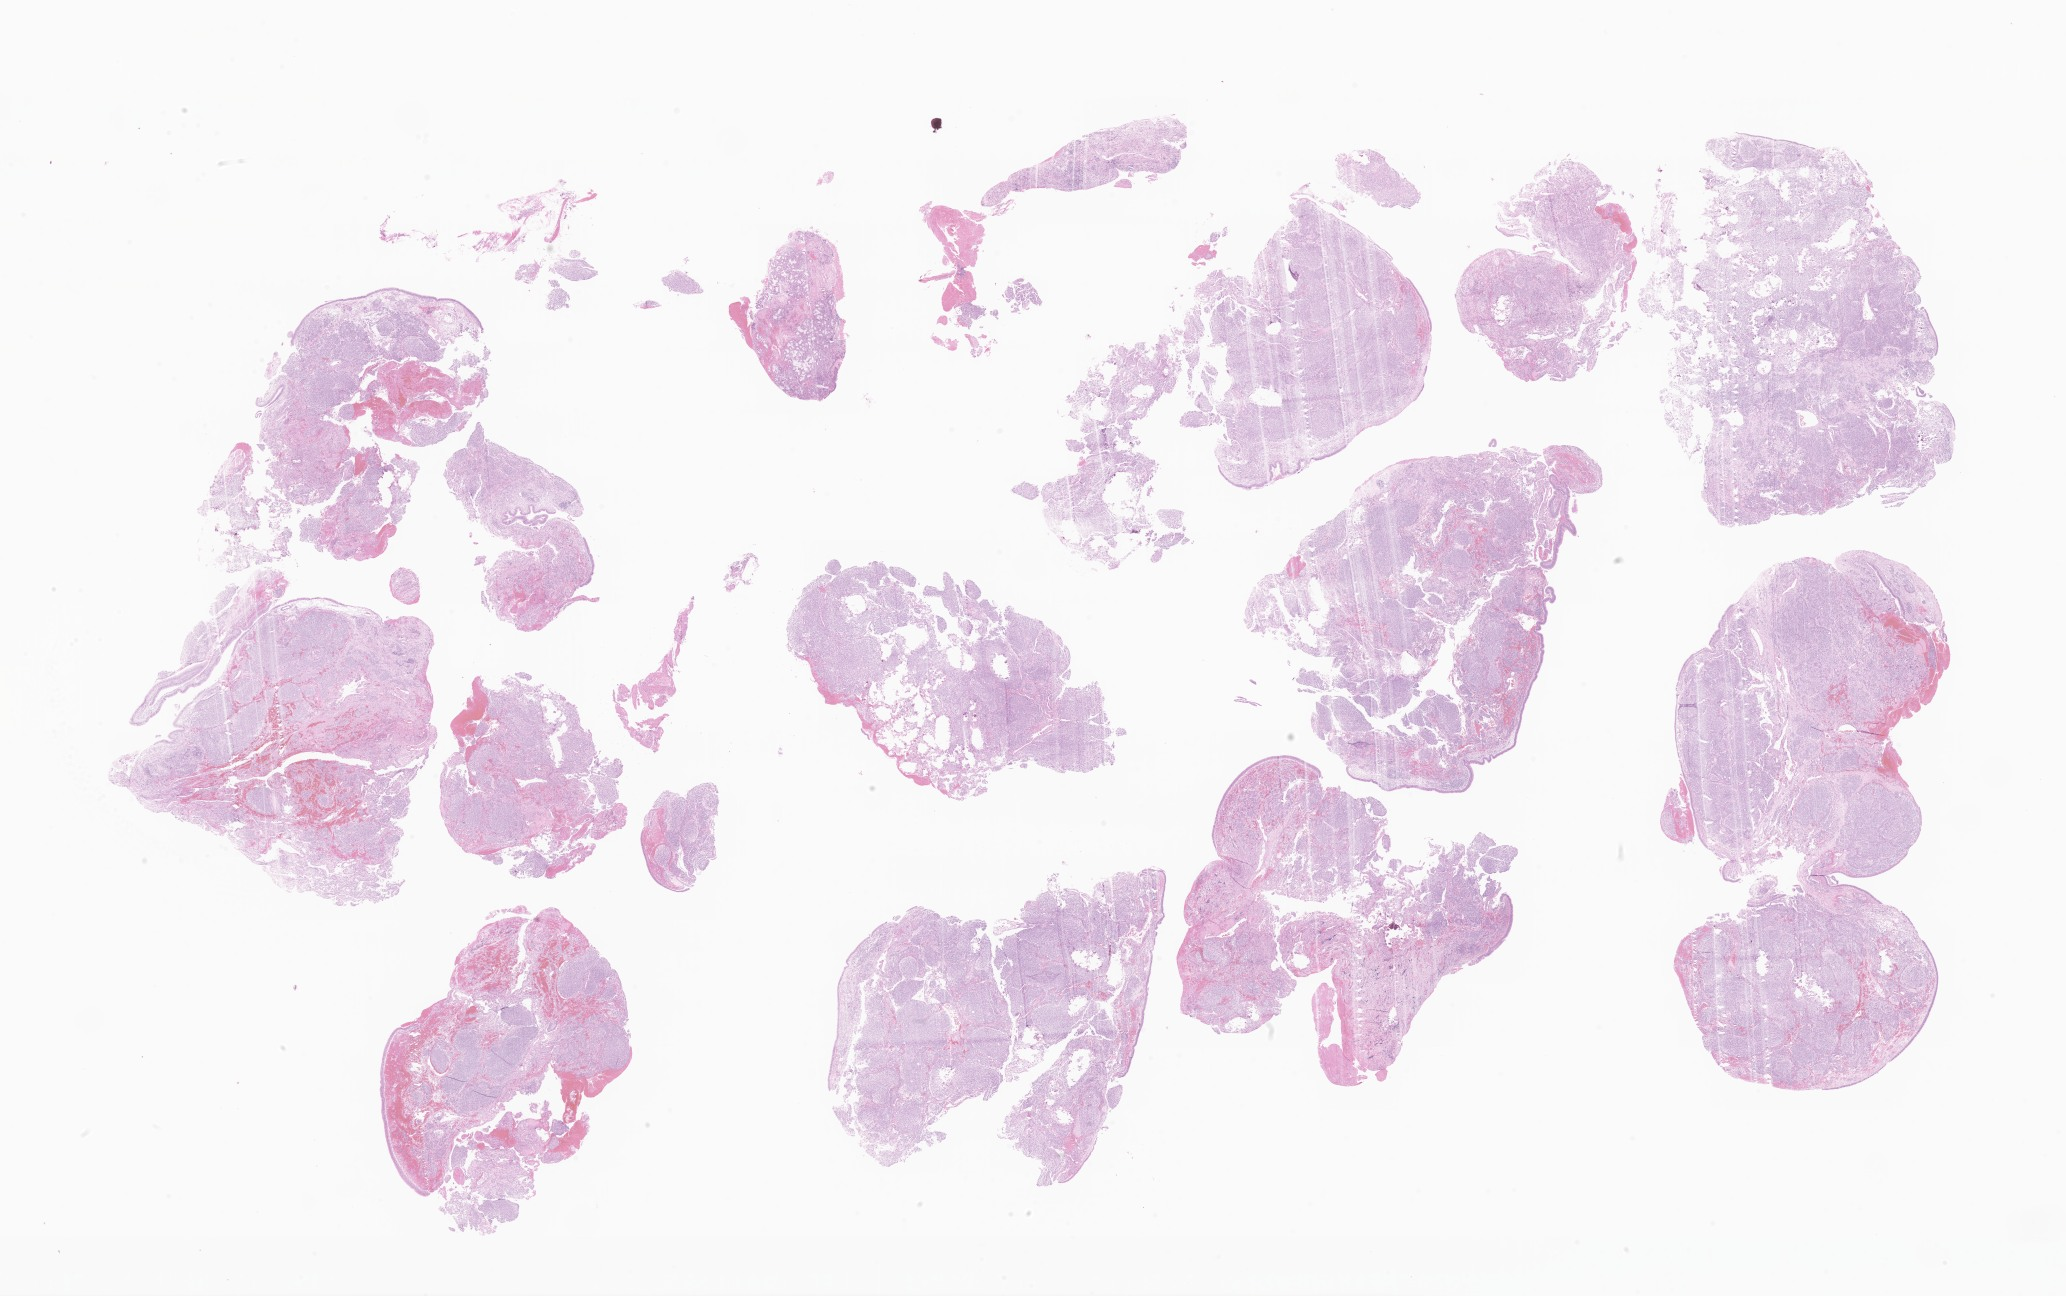
Digitized H&E-stained section of tumor tissue from the maxillary sinus — a low-resolution overview of the entire scanned area, about 34.8 x 21.9 mm; FFPE section. Patient male; age 154 months (12 years 10 months).
Diagnosis: Olfactory neuroblastoma.